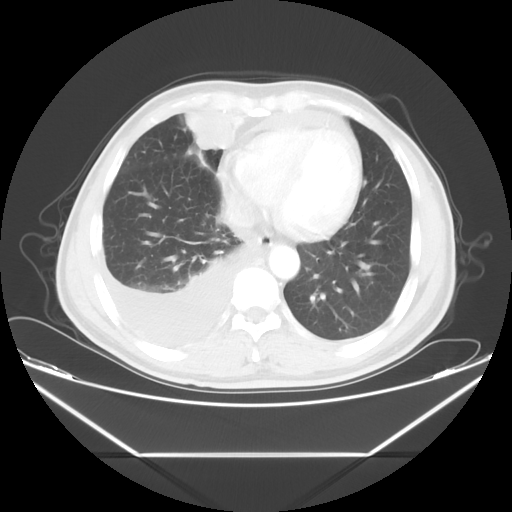
Chest CT, one axial slice; slice 17 of 56 in the series (ordered by position); reconstruction kernel STANDARD; 120 kVp; lung window (W 1500 / L -600 HU); 5 mm slice thickness; 512 × 512 image matrix. Patient: male, 57 years. From the clinical record (not read from this slice): clinical TNM (as recorded): T2 N3 M1.
Annotated regions visible in this slice (bounding box drawn by a radiologist):
- lung tumour (recorded histology: adenocarcinoma): bounding box [x1, y1, x2, y2] px = [184, 108, 239, 154]